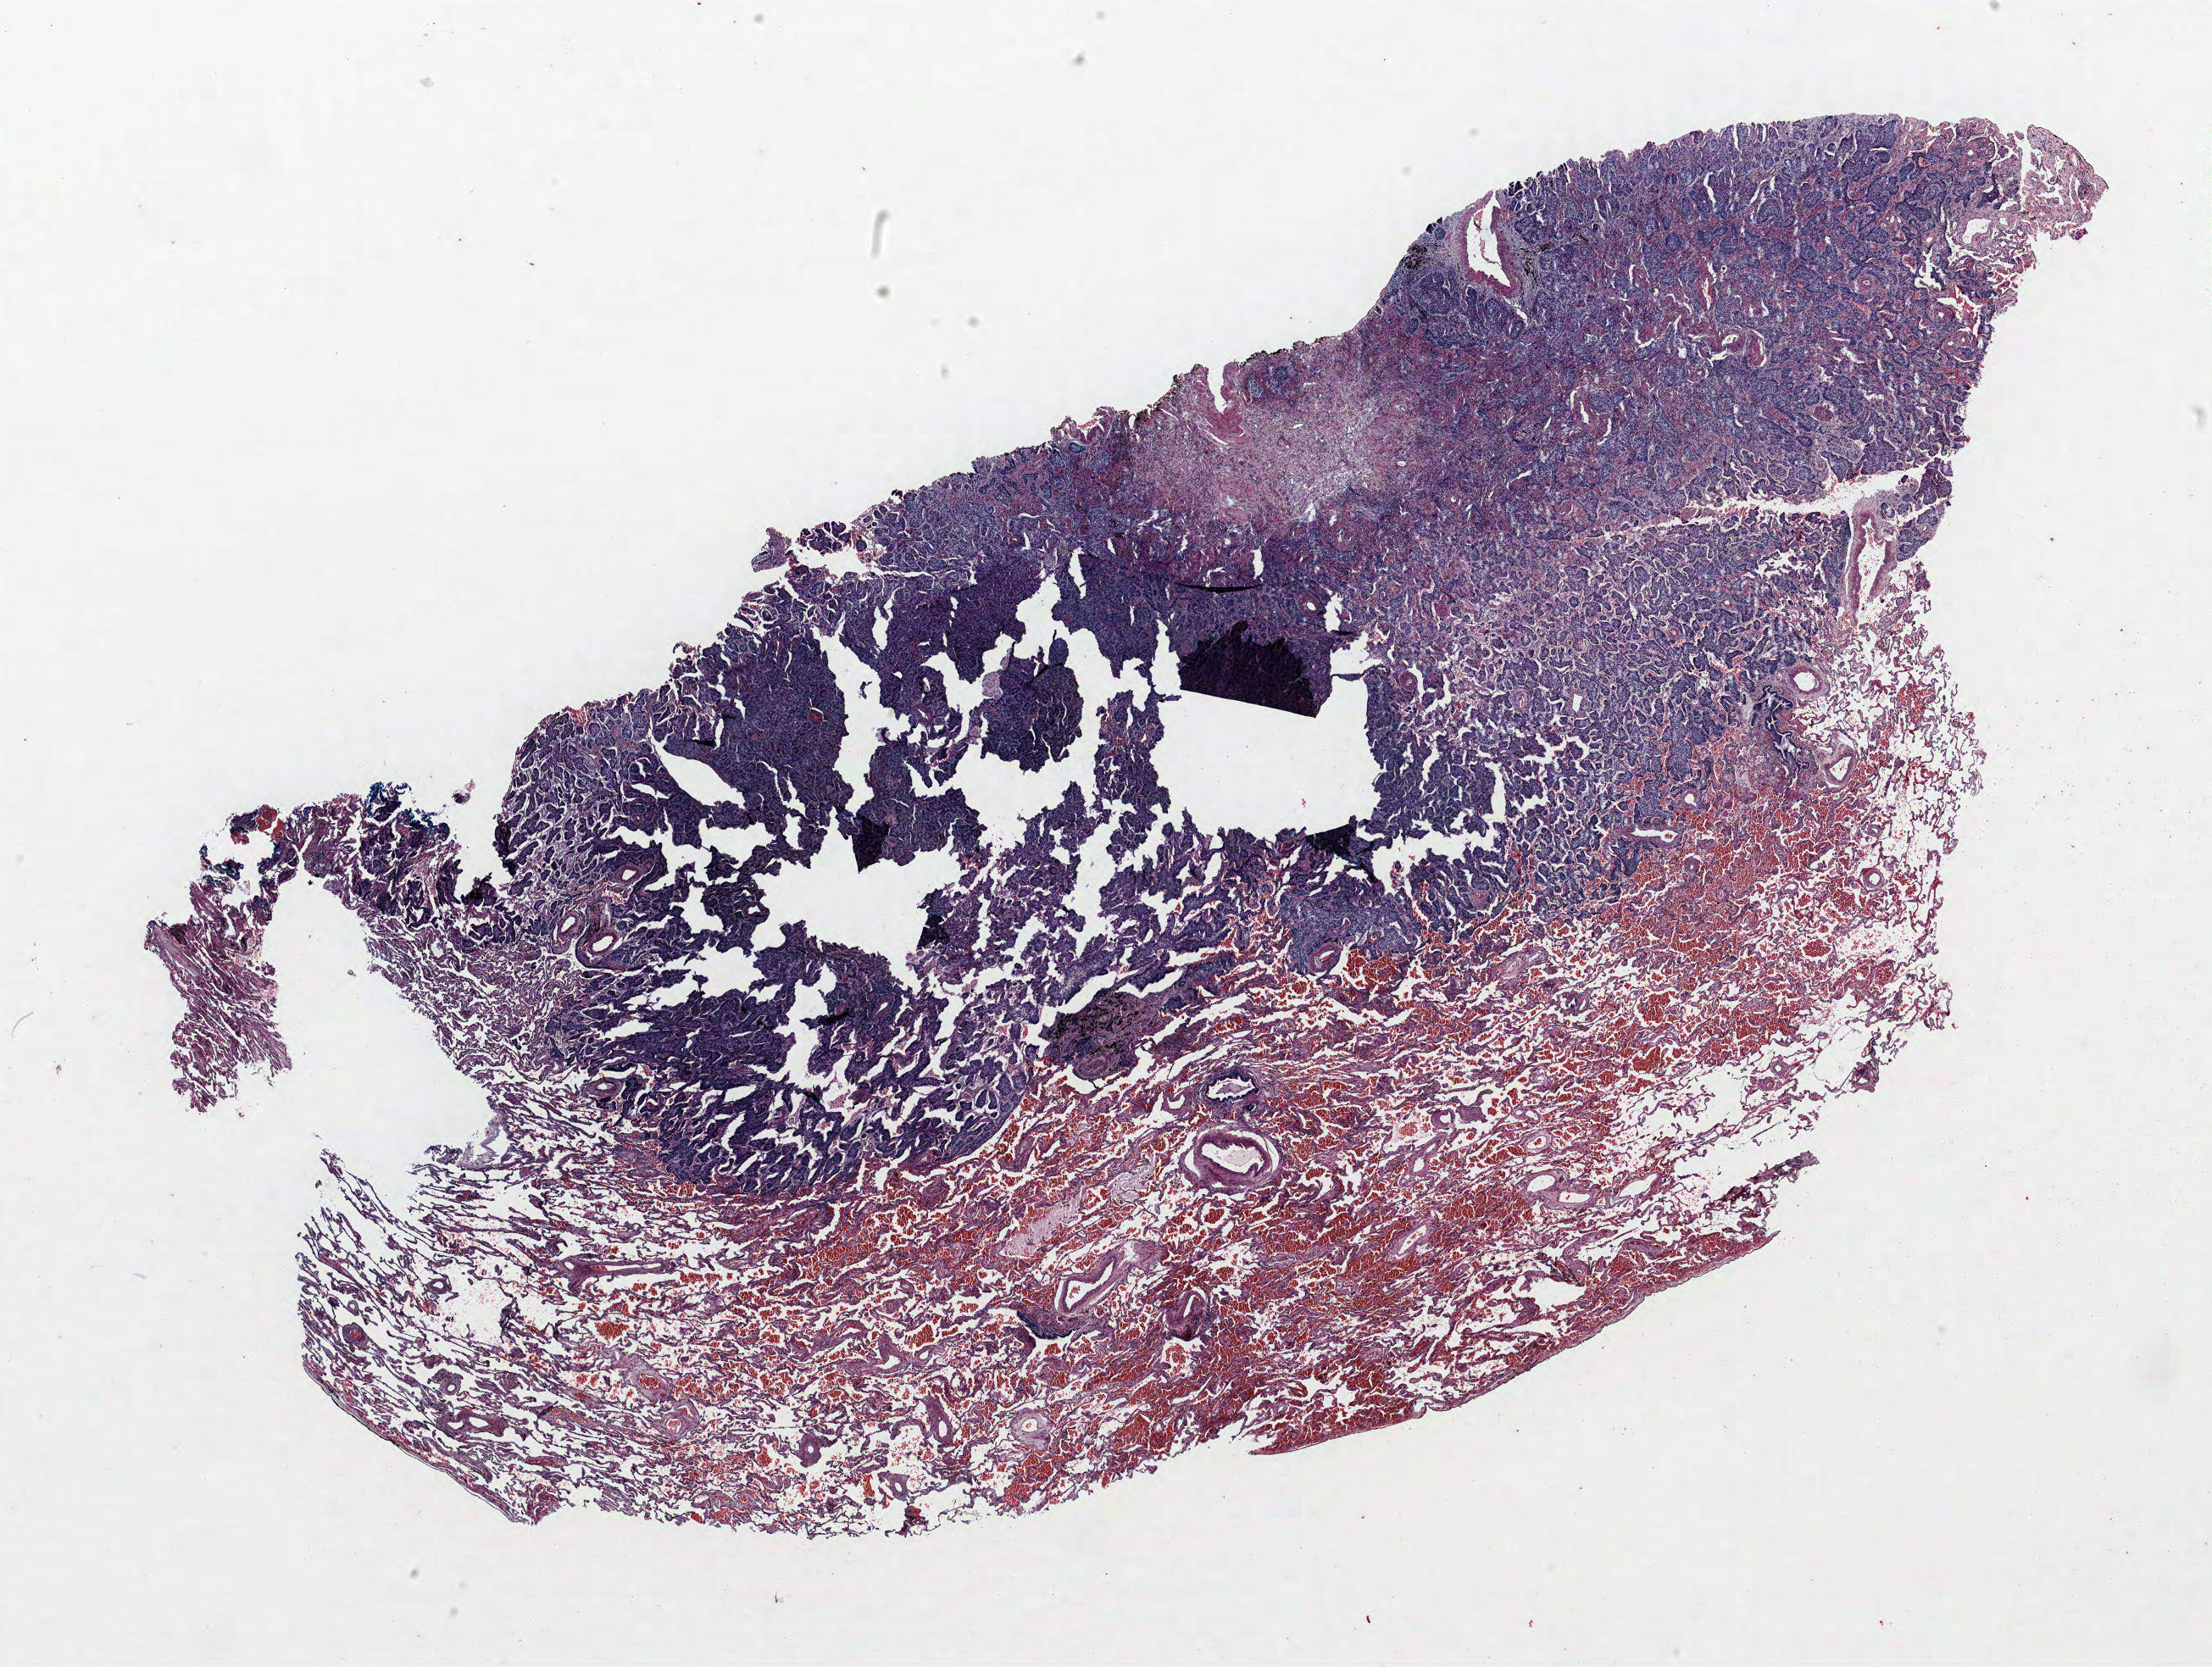
H&E-stained whole-slide image, shown as a low-resolution overview of the whole scanned area (about 20.9 x 15.7 mm, slide scanned at 40x). Formalin-fixed paraffin-embedded (FFPE) section. Lung tissue. Male patient, aged 70 at enrolment. Current smoker at enrolment. Grade: poorly differentiated (G3).
* tumour size (pathology): 24 mm
* primary tumour location (clinical record): right lower lobe
* stage (AJCC 6th edition): IB
* participant's lung-cancer diagnosis: Squamous cell carcinoma, NOS